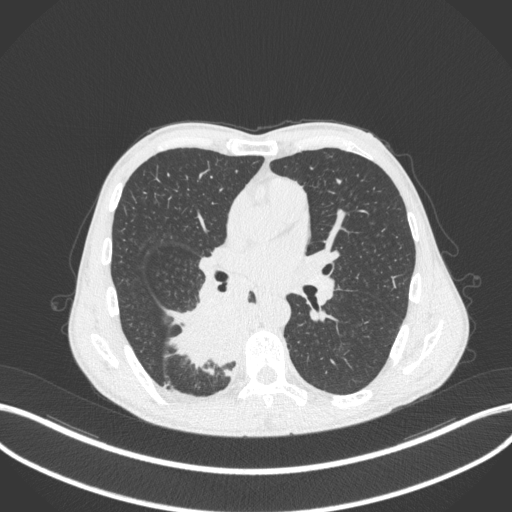
Chest CT, one axial slice; position 199 of 371 along the scan axis; 120 kVp; lung window (W 1500 / L -600 HU); 512 × 512 image matrix. Male patient, age 58 years. Case-level facts recorded for this patient, not image findings: clinical TNM (as recorded): T3 N1 M1.
Annotated regions visible in this slice (rectangle marked by the reading radiologist):
- lung tumour (recorded histology: squamous cell carcinoma): bounding box (x1, y1, x2, y2) in pixels: (162, 282, 253, 372)